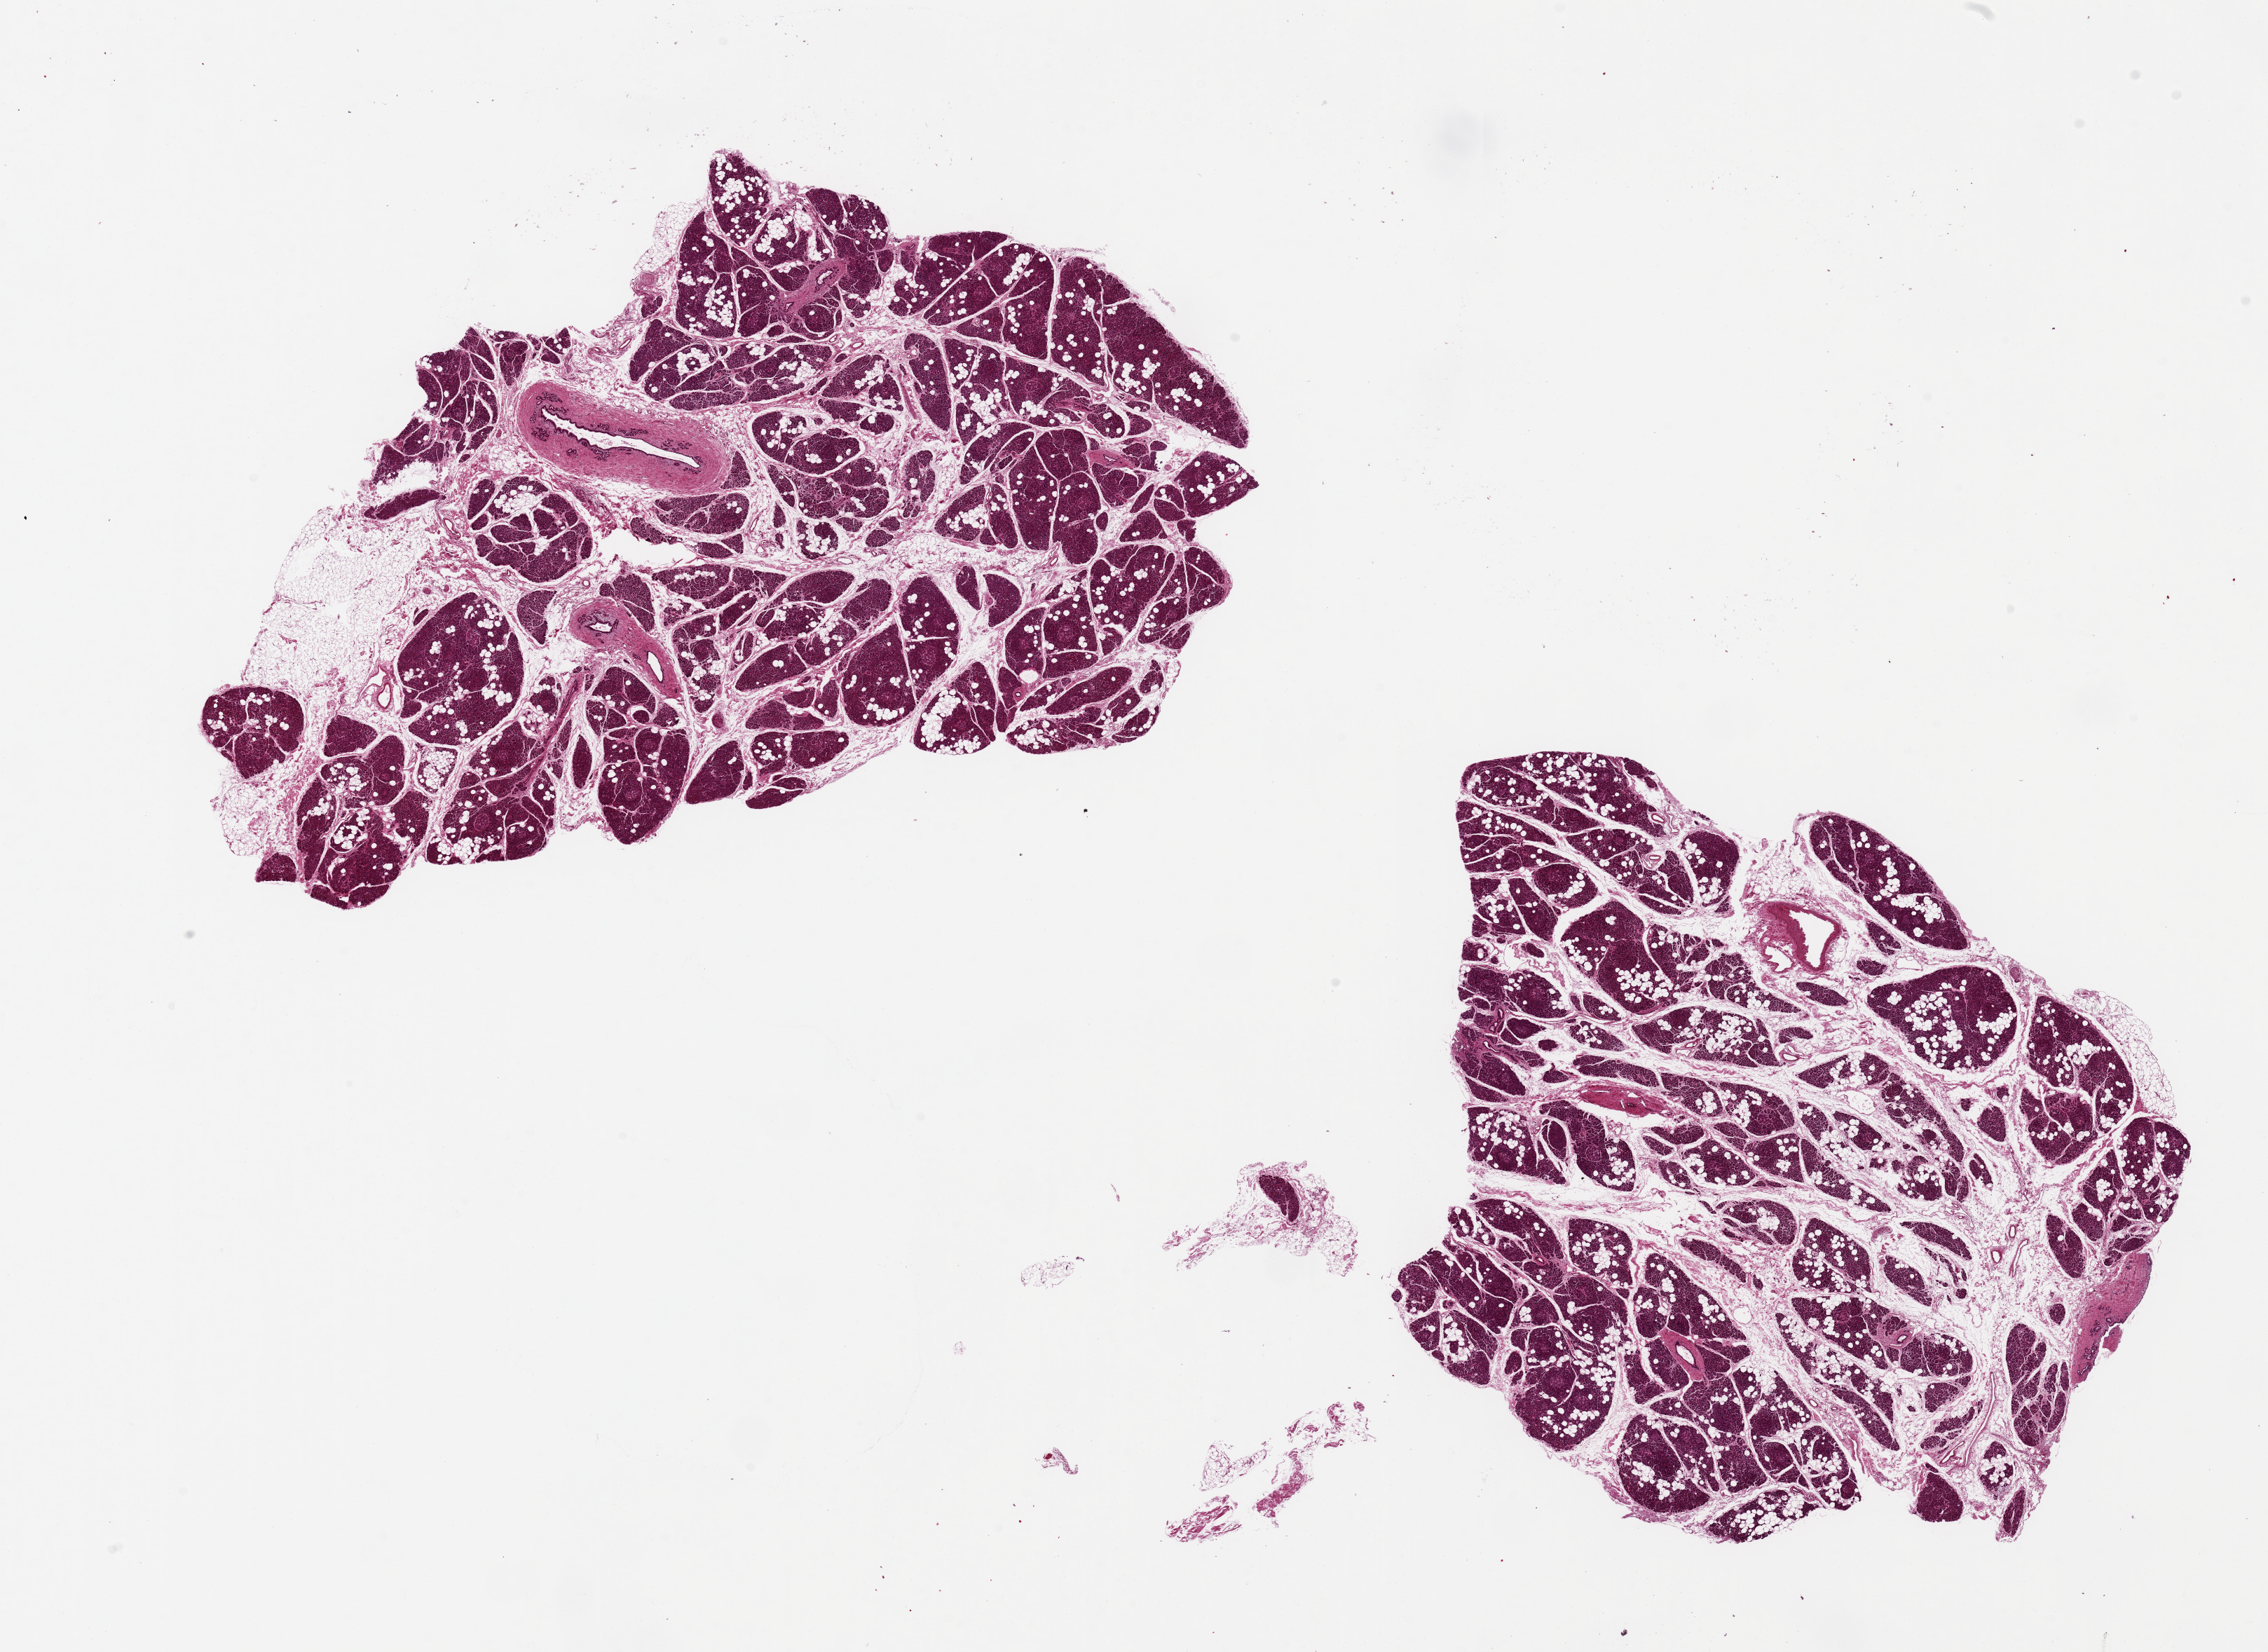
Digitized hematoxylin and eosin (H&E)-stained section, a low-resolution overview of the entire scanned area, about 25.6 x 18.6 mm (acquisition: 20x scan). PAXgene-fixed, paraffin-embedded tissue. Sampled site (target tissue): pancreas. Tissue donor sample. Donor: female.
Pathologist's review note for this sample: 2 pieces, ~8x8mm, Islets of Langherhans viislble.